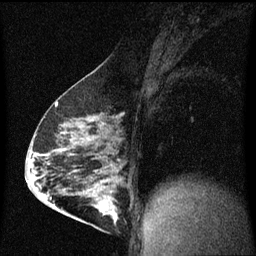
Breast MRI (dynamic contrast-enhanced), one sagittal slice. Position 33 of 60 along the scan axis. Dynamic contrast-enhanced series, image 2 of 3 at this slice position (ordered by acquisition). 1.5 T. TE 4.2 ms, TR 8 ms. 2 mm slice thickness. 256 × 256 image matrix, field of view 200 × 200 mm. Patient: female, 63 years.
Annotated regions visible in this slice (semi-automatic segmentation, software-assisted and operator-edited):
- analysis volume of interest (the breast-tissue region the enhancement analysis was run in; not a lesion): box from (x=88, y=182) to (x=125, y=229) px
- tumour enhancement mask (voxels above the 70 % enhancement threshold inside the analysis volume of interest): (x=96, y=182)–(x=117, y=223)